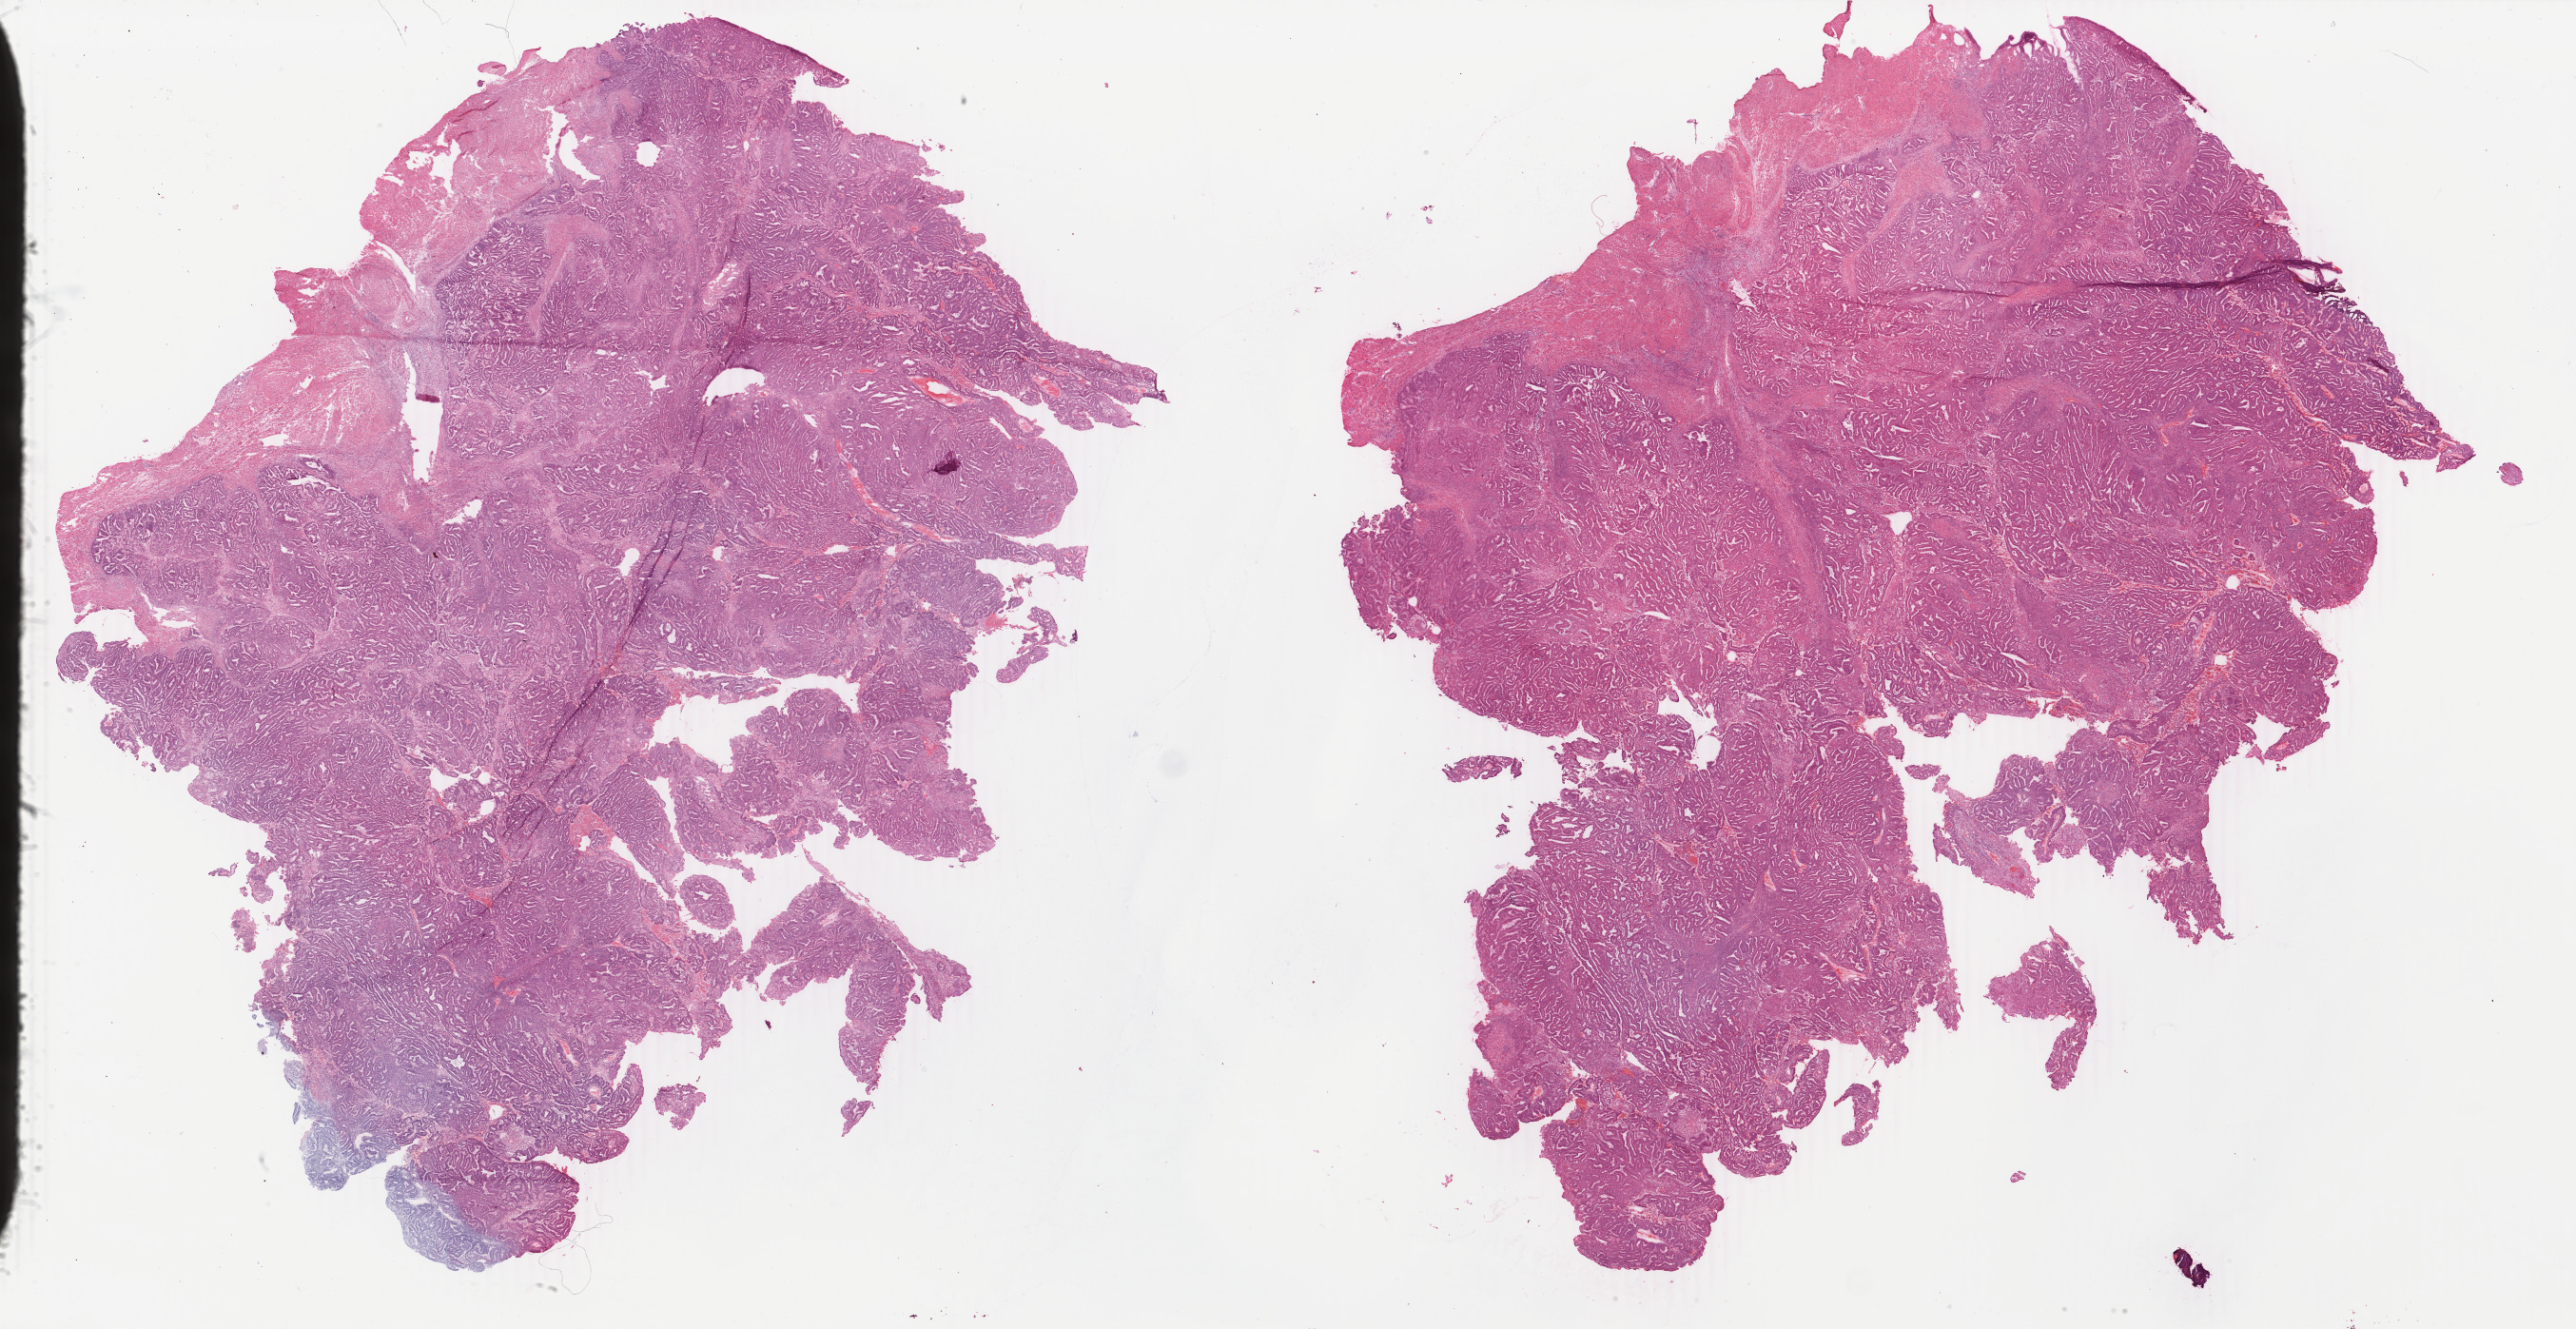
H&E whole-slide image — whole scanned area (about 43.1 x 22.2 mm, acquisition: 40x scan) shown as a low-resolution overview. FFPE section. Primary tumour sample from the uterus. Female, age 63 years at initial diagnosis. Histologic grade: G2 (moderately differentiated).
• histologic diagnosis: Endometrioid adenocarcinoma, NOS
• FIGO stage: IIB